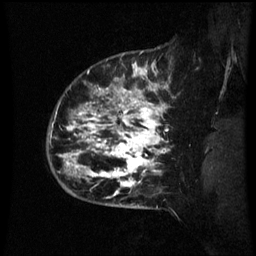
Breast MRI (dynamic contrast-enhanced), one sagittal slice. Slice 53 of 60 in the series (ordered by position). Dynamic contrast-enhanced series, image 2 of 3 at this slice position (ordered by acquisition). 1.5 T. TE 4.2 ms, TR 8.9 ms. 2.1 mm slice thickness. 256 × 256 image matrix, field of view 200 × 200 mm. Patient: female, 42 years. Case-level facts recorded for this patient, not image findings: setting: breast cancer imaged before/during neoadjuvant chemotherapy; receptor status: HER2-positive.
Structures marked on this image (semi-automatically segmented with operator editing):
- analysis volume of interest (the breast-tissue region the enhancement analysis was run in; not a lesion): bounding box (x1, y1, x2, y2) in pixels: (66, 82, 173, 193)
- tumour enhancement mask (voxels above the 70 % enhancement threshold inside the analysis volume of interest): (66, 84, 169, 193)